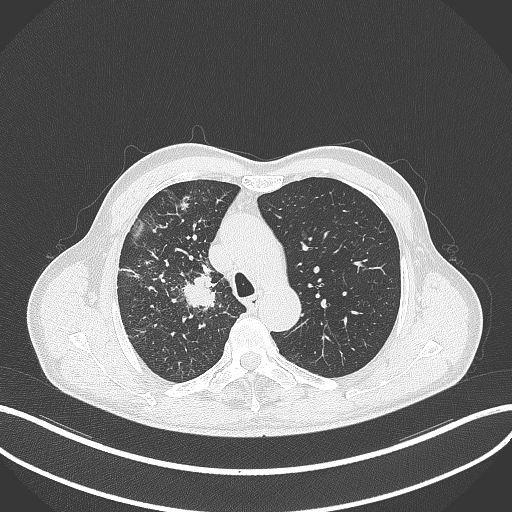
Chest CT, one axial slice. Slice 352 of 490 in the series (ordered by position). 120 kVp. Lung window (W 1500 / L -600 HU). 1 mm slice thickness. 512 × 512 image matrix, field of view 400 × 400 mm. Patient: male, 69 years. Case-level facts recorded for this patient, not image findings: clinical TNM (as recorded): T2a N0 M0.
Outlined on this slice (rectangle marked by the reading radiologist):
- lung tumour (recorded histology: adenocarcinoma): bounding box (x1, y1, x2, y2) in pixels: (179, 270, 225, 311)